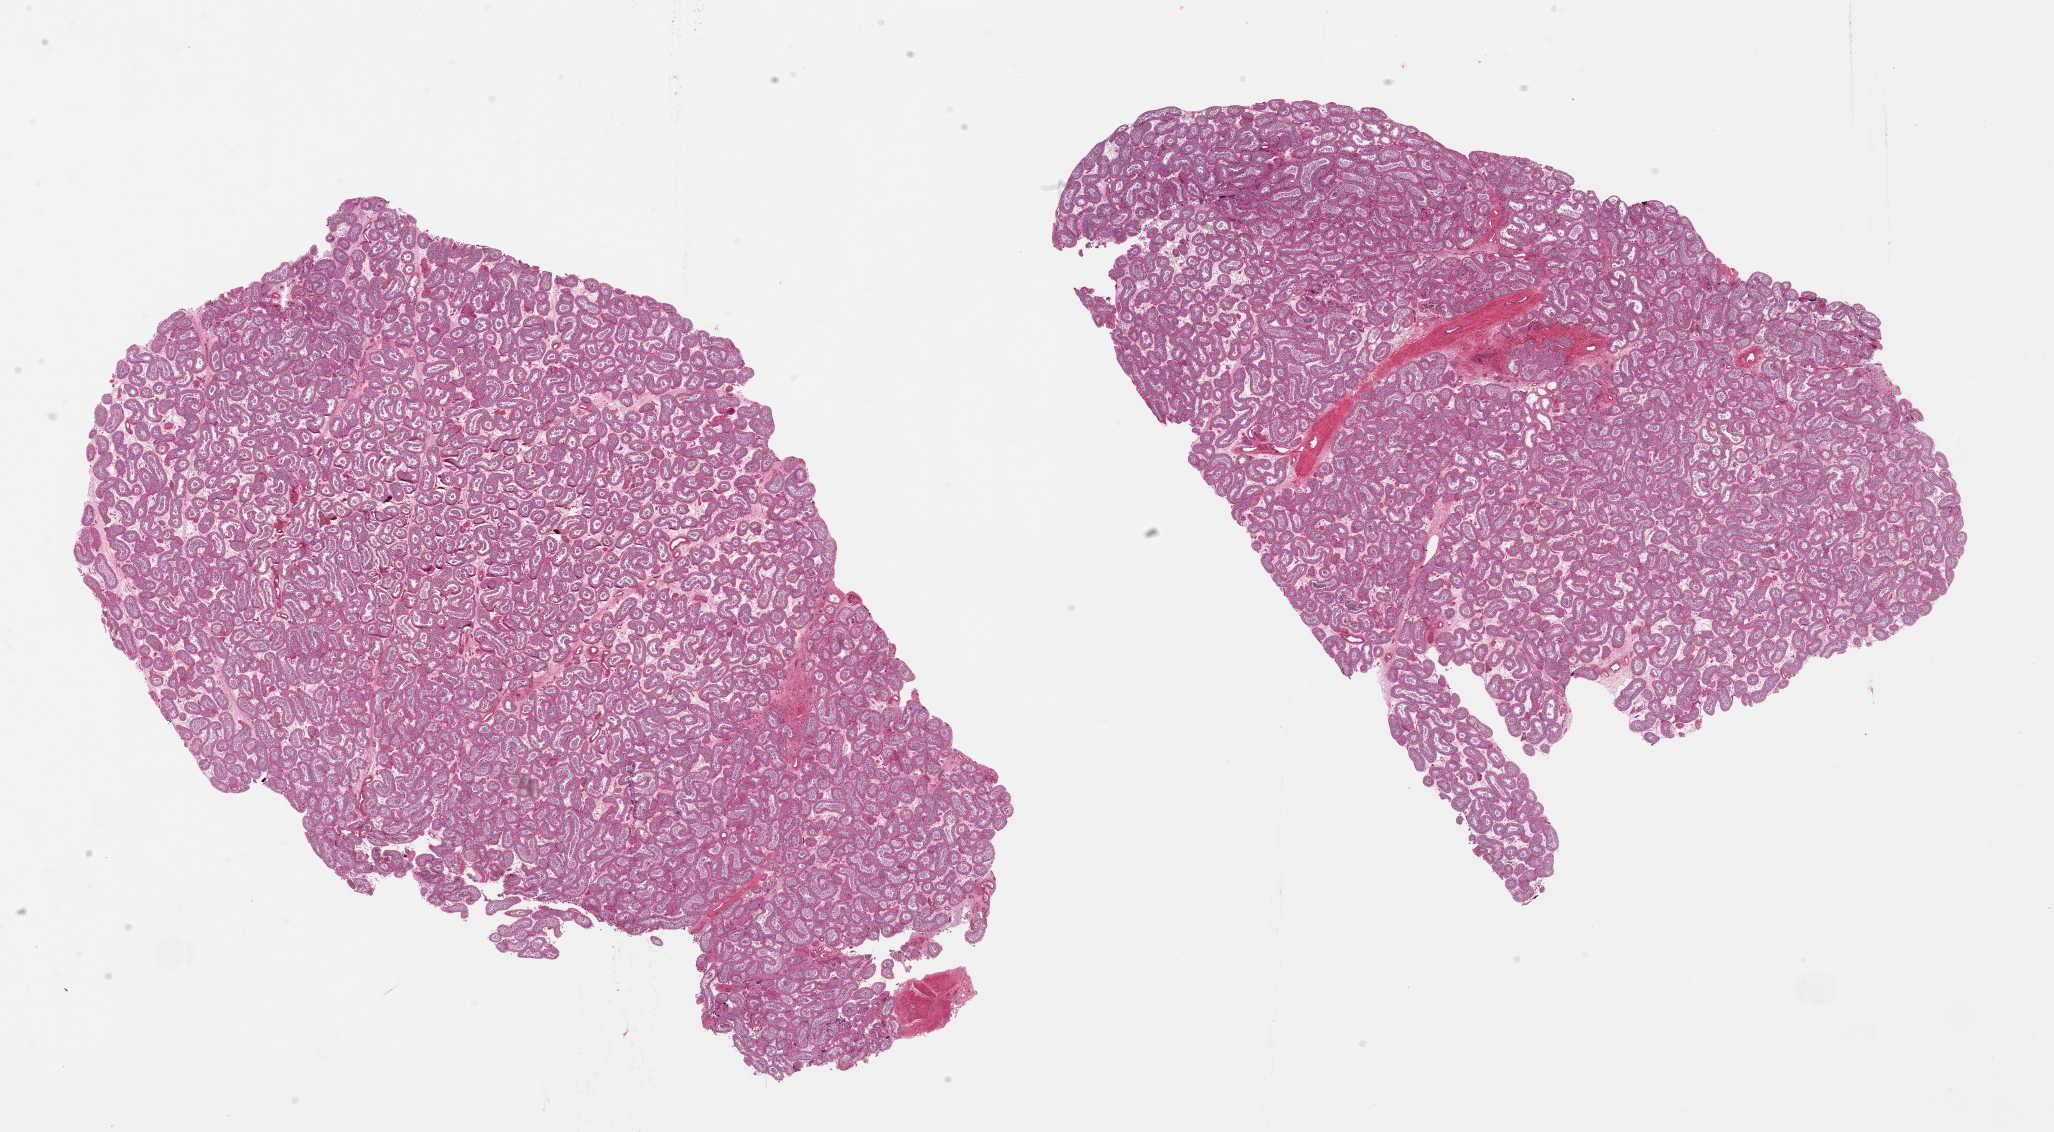
H&E whole-slide image, brightfield — a low-resolution overview of the entire scanned area, about 32.5 x 17.9 mm, PAXgene-fixed paraffin-embedded (PFPE) section, section of testis (target tissue), tissue donor sample. Donor: male.
Reviewer comment on this tissue sample: 2 pieces, active spermatogenesis.